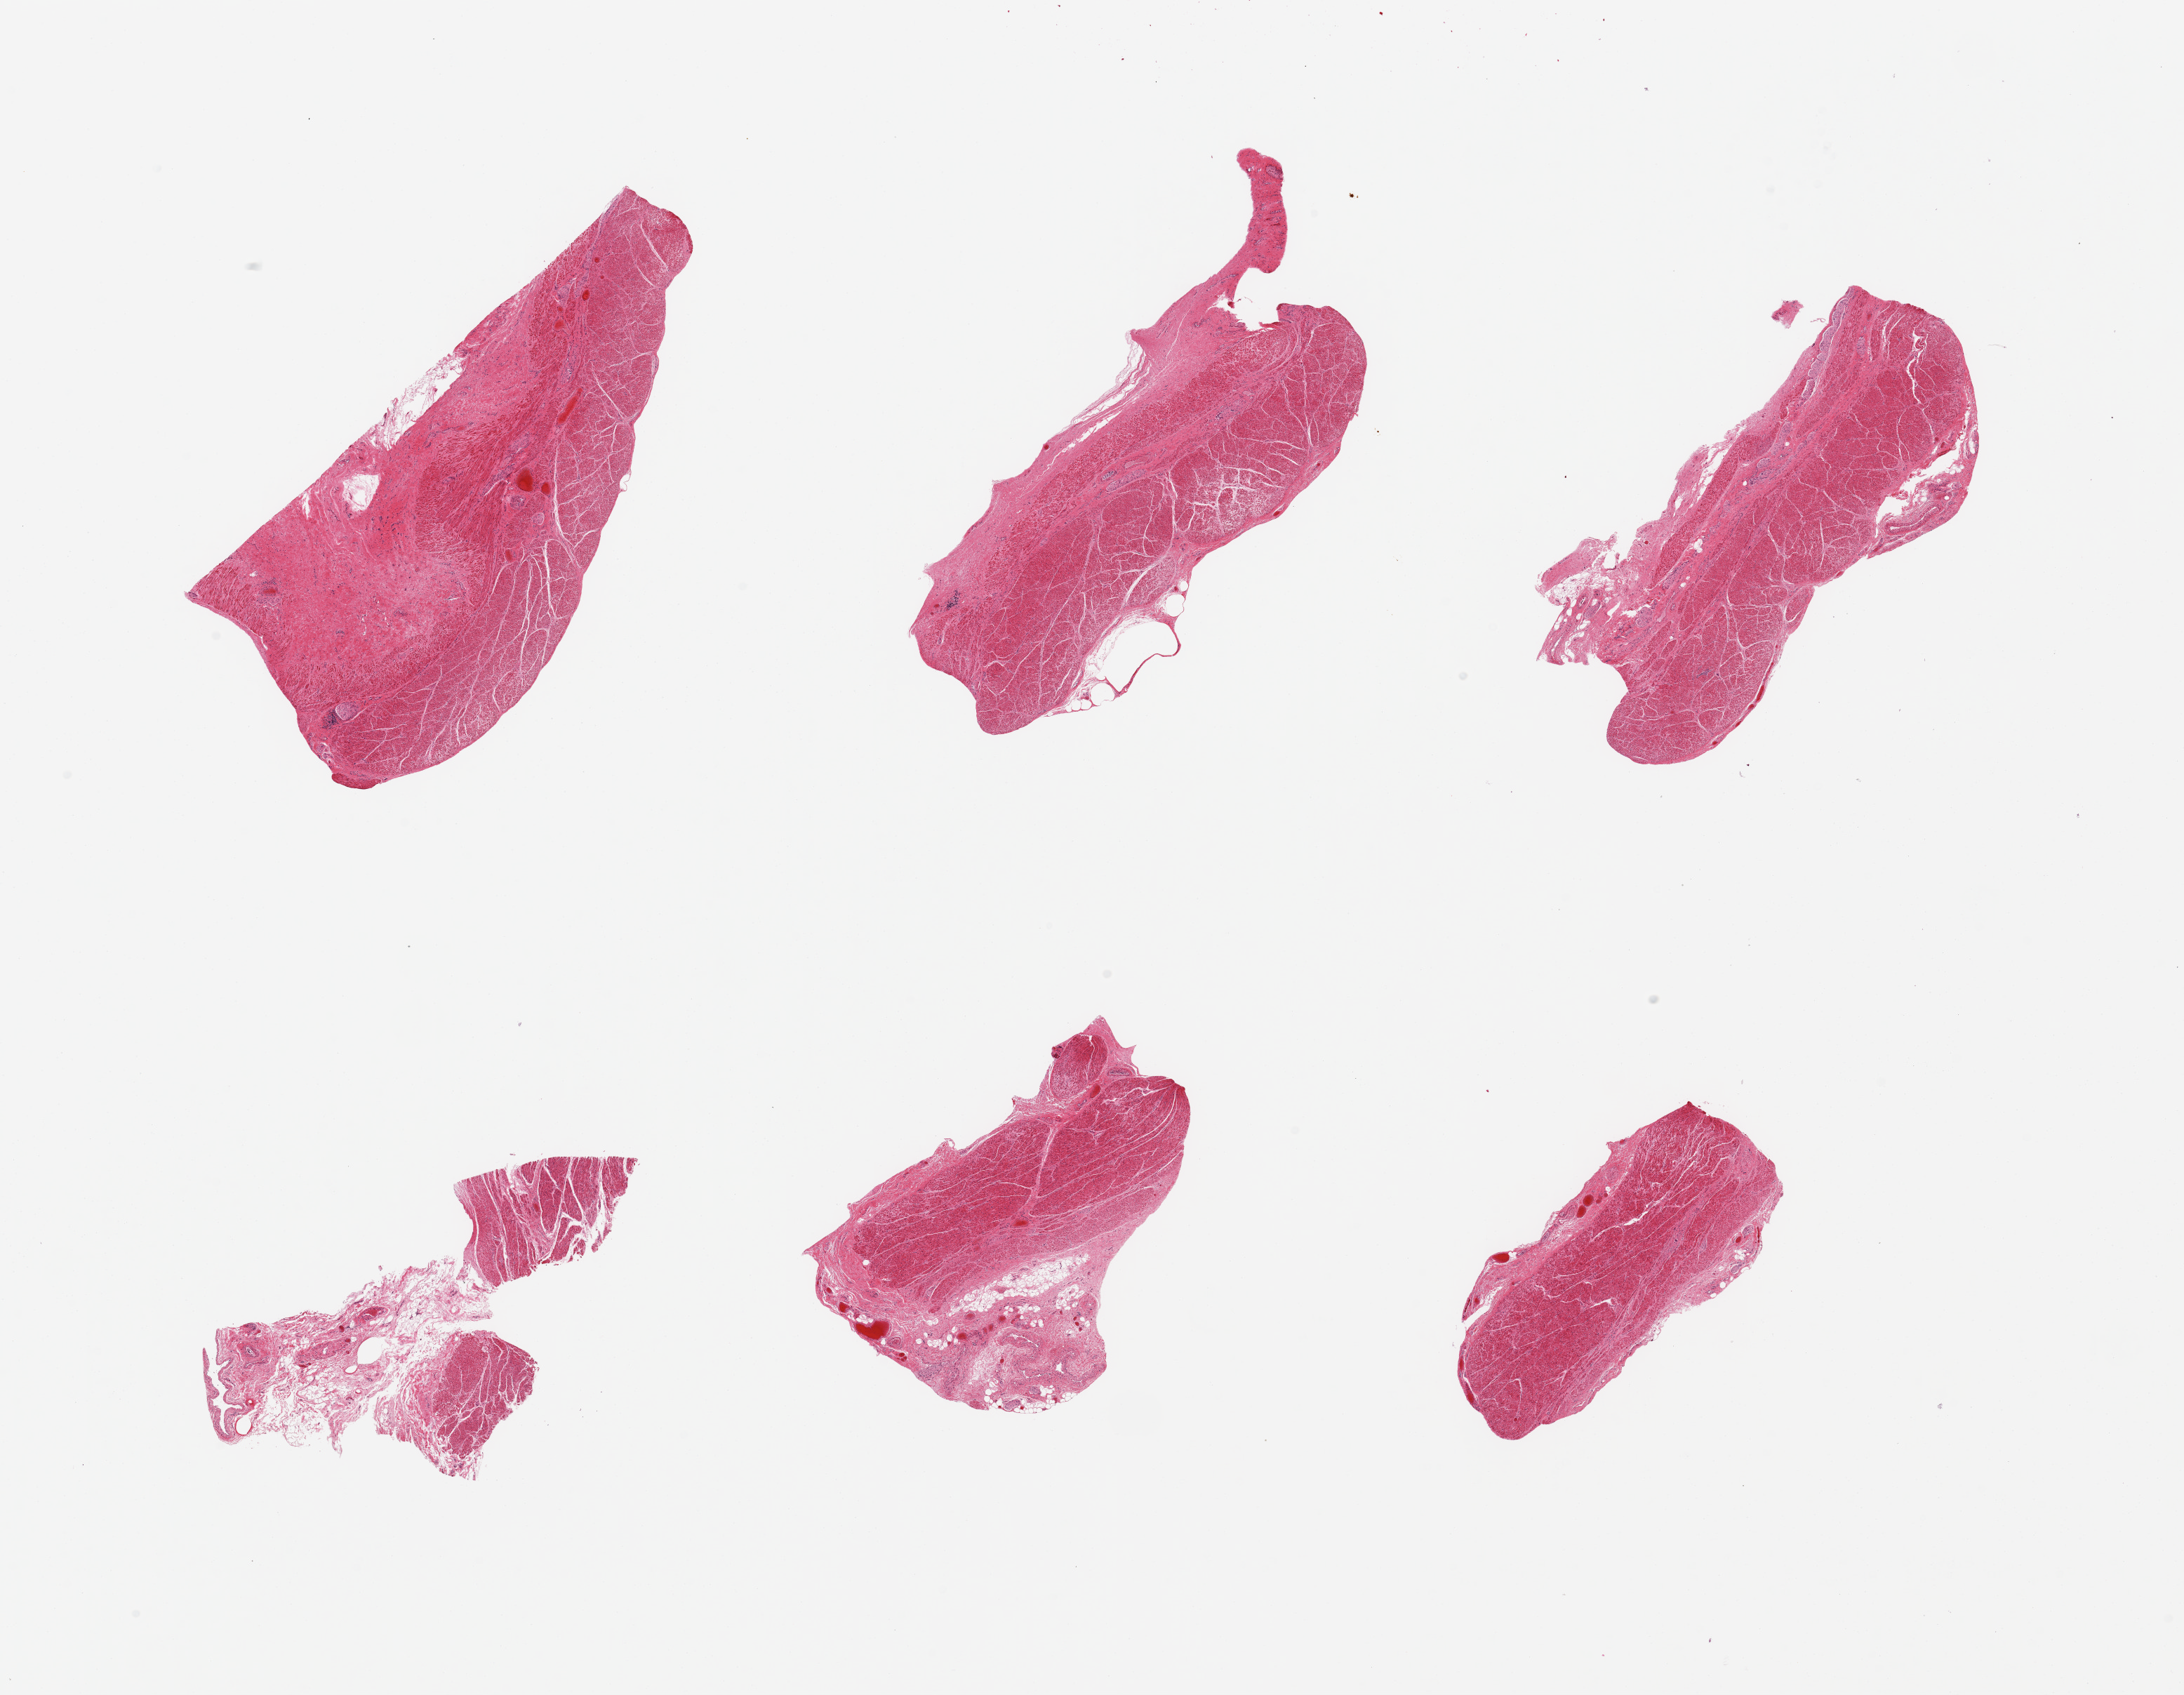
Whole-slide image, H&E stain — shown as a low-resolution overview of the whole scanned area (about 24.6 x 19.1 mm, from a 20x scan). PAXgene-fixed, paraffin-embedded tissue. Sampled site (target tissue): gastroesophageal junction. Tissue donor sample. Donor: female.
Reviewer comment on this tissue sample: 6 pieces; predominantly muscularis, some with attached submucosa/adventitia.